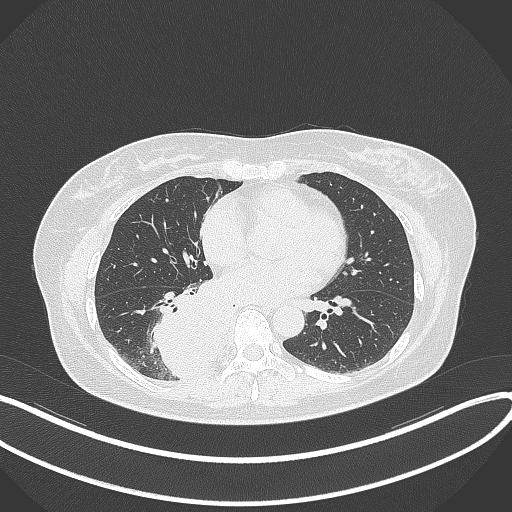
Chest CT, one axial slice. Position 156 of 331 along the scan axis. 120 kVp. Lung window (W 1500 / L -600 HU). 1 mm slice thickness. 512 × 512 image matrix, field of view 400 × 400 mm. Patient: female, 54 years. Case-level facts recorded for this patient, not image findings: clinical TNM (as recorded): T4 N0 M0.
Structures marked on this image (rectangle marked by the reading radiologist):
- lung tumour (recorded histology: adenocarcinoma): box from (x=148, y=277) to (x=233, y=378) px